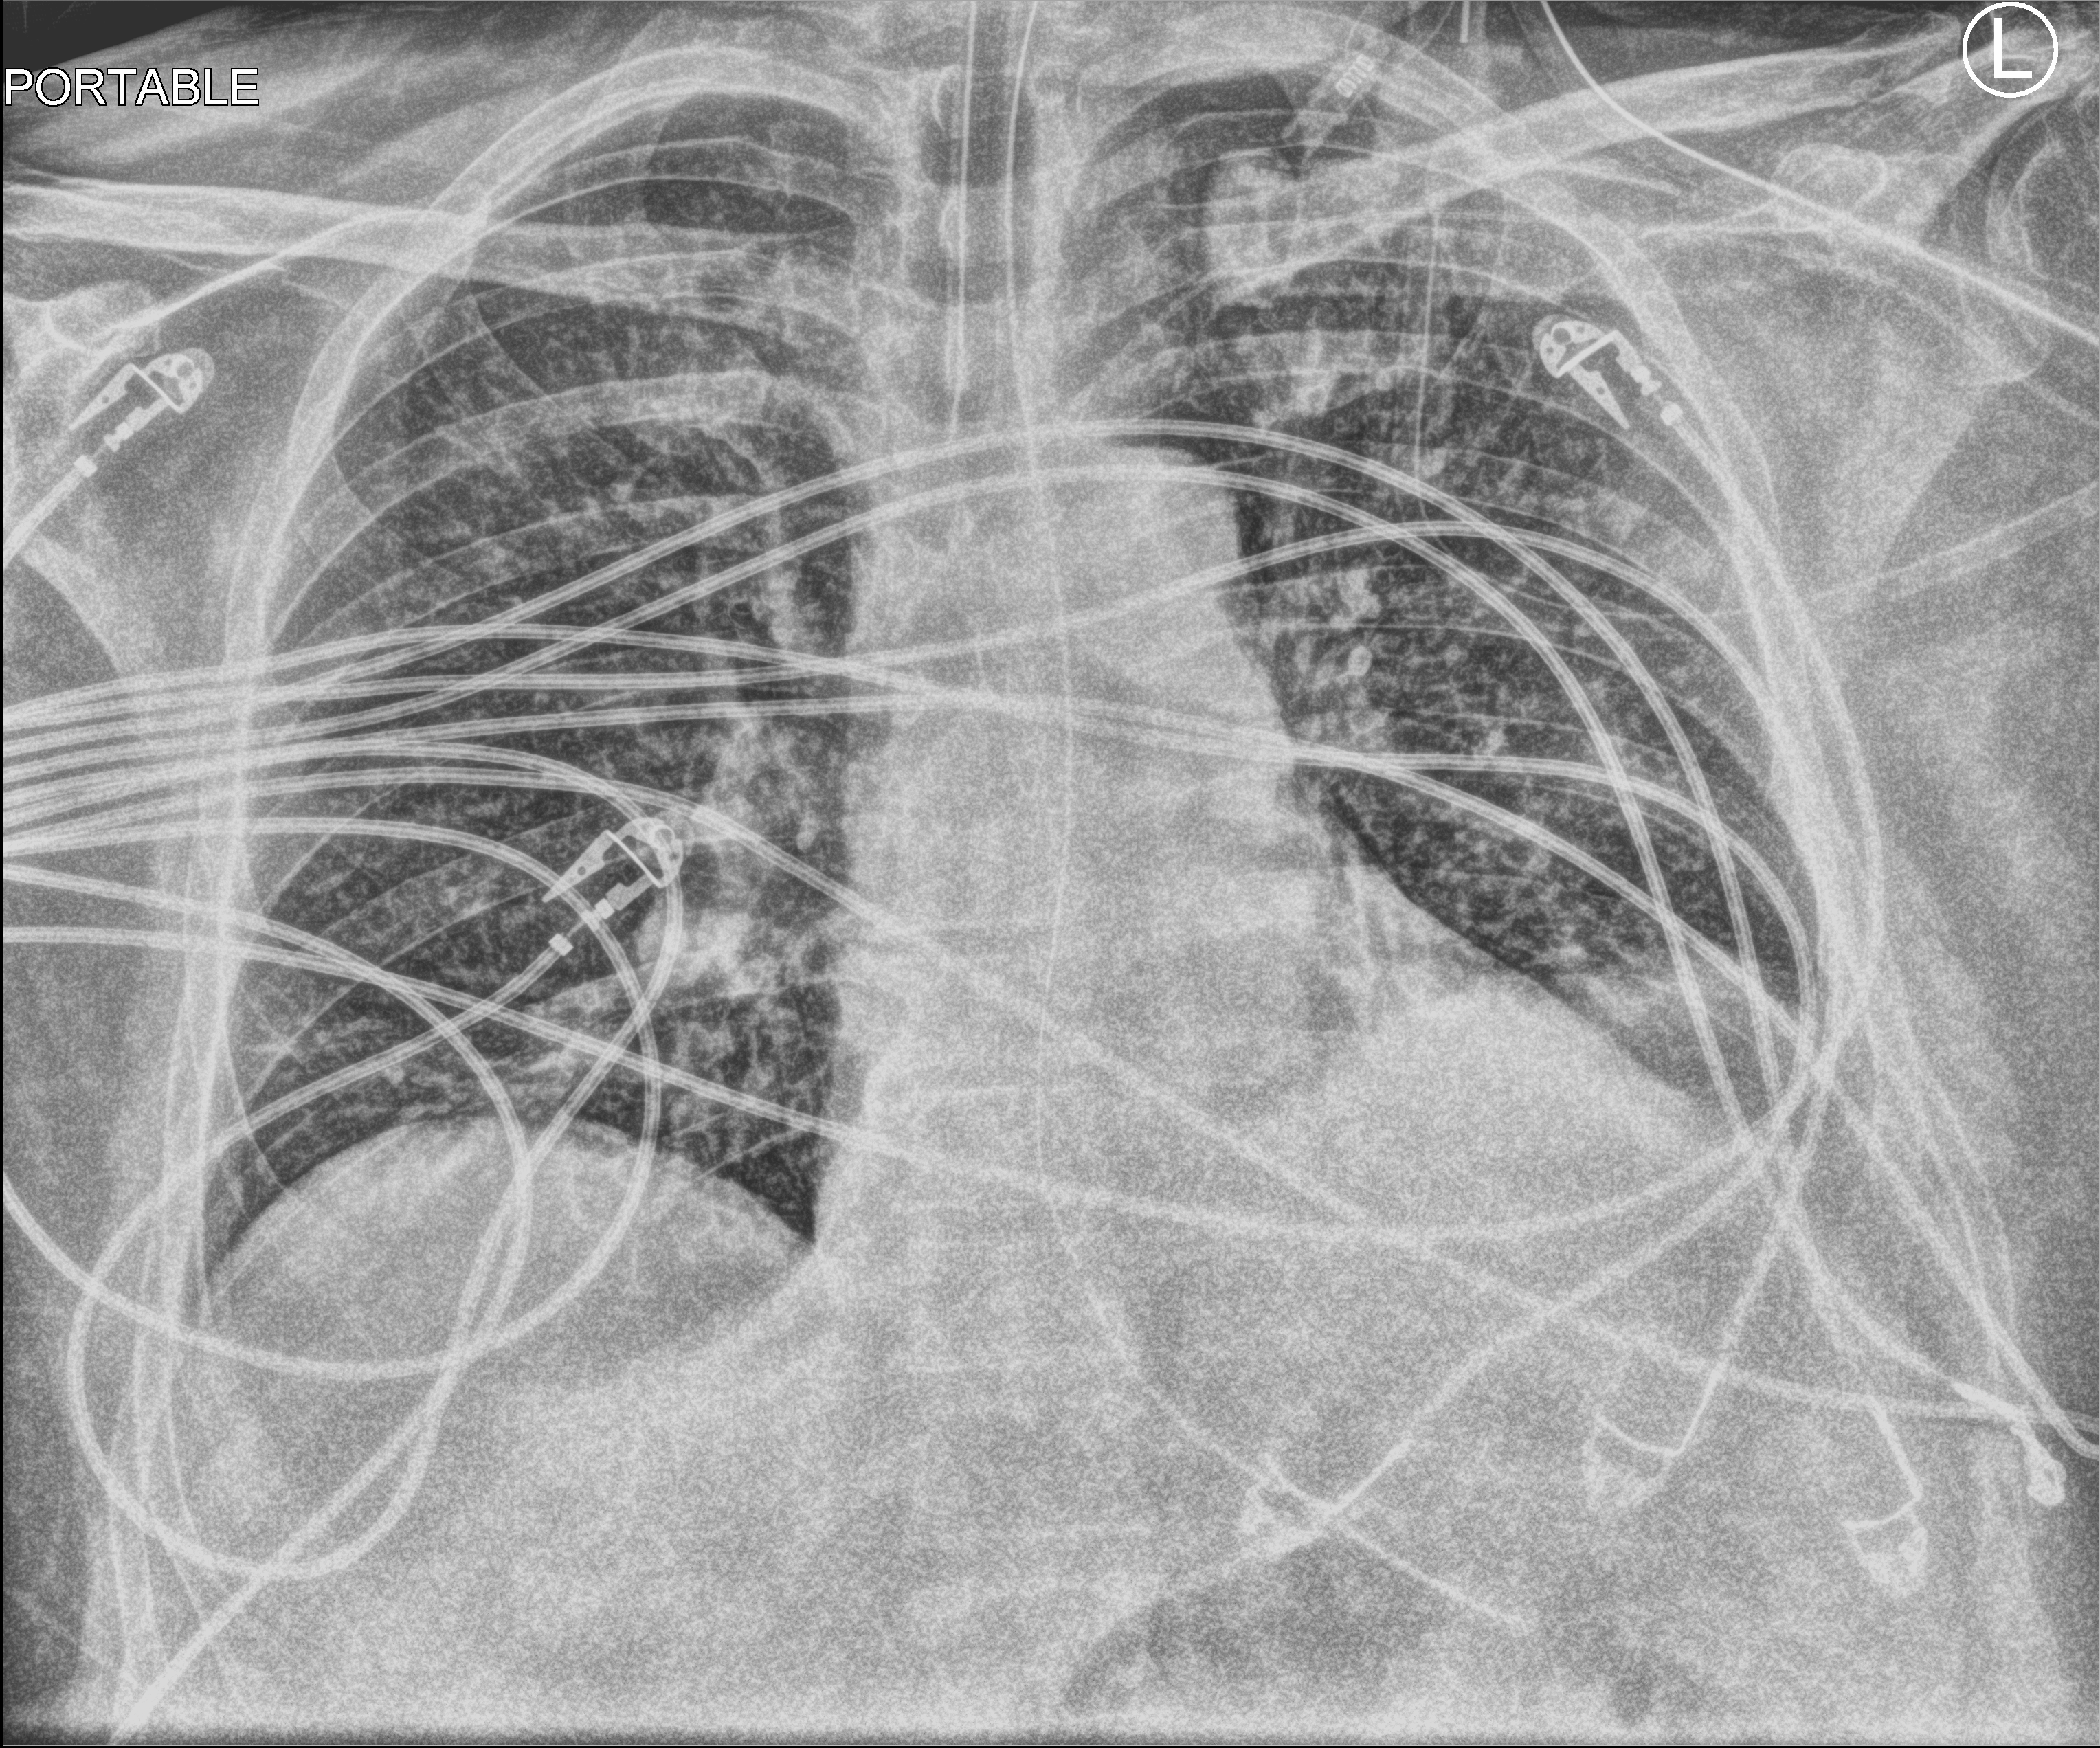
Portable chest radiograph, anteroposterior (AP) projection. Male patient hospitalised with COVID-19, age 60–74 years.
Hospital-stay facts (about this admission, not read from this image; timing relative to this image not recorded): admitted to intensive care during this hospital stay: yes; mechanically ventilated during this hospital stay: yes.